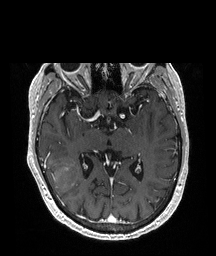
Brain MRI from a brain-tumour surgery series, one axial slice. Position 118 of 208 along the scan axis. T1-weighted post-contrast. 1 mm slice thickness. 216 × 256 image matrix, field of view 216 × 256 mm. From the clinical record (not read from this slice): histopathology: Glioblastoma; WHO grade: 4; IDH mutation: no.
Annotated regions visible in this slice (outlined manually by an expert reader):
- tumour: bounding box [x1, y1, x2, y2] px = [45, 156, 77, 193]